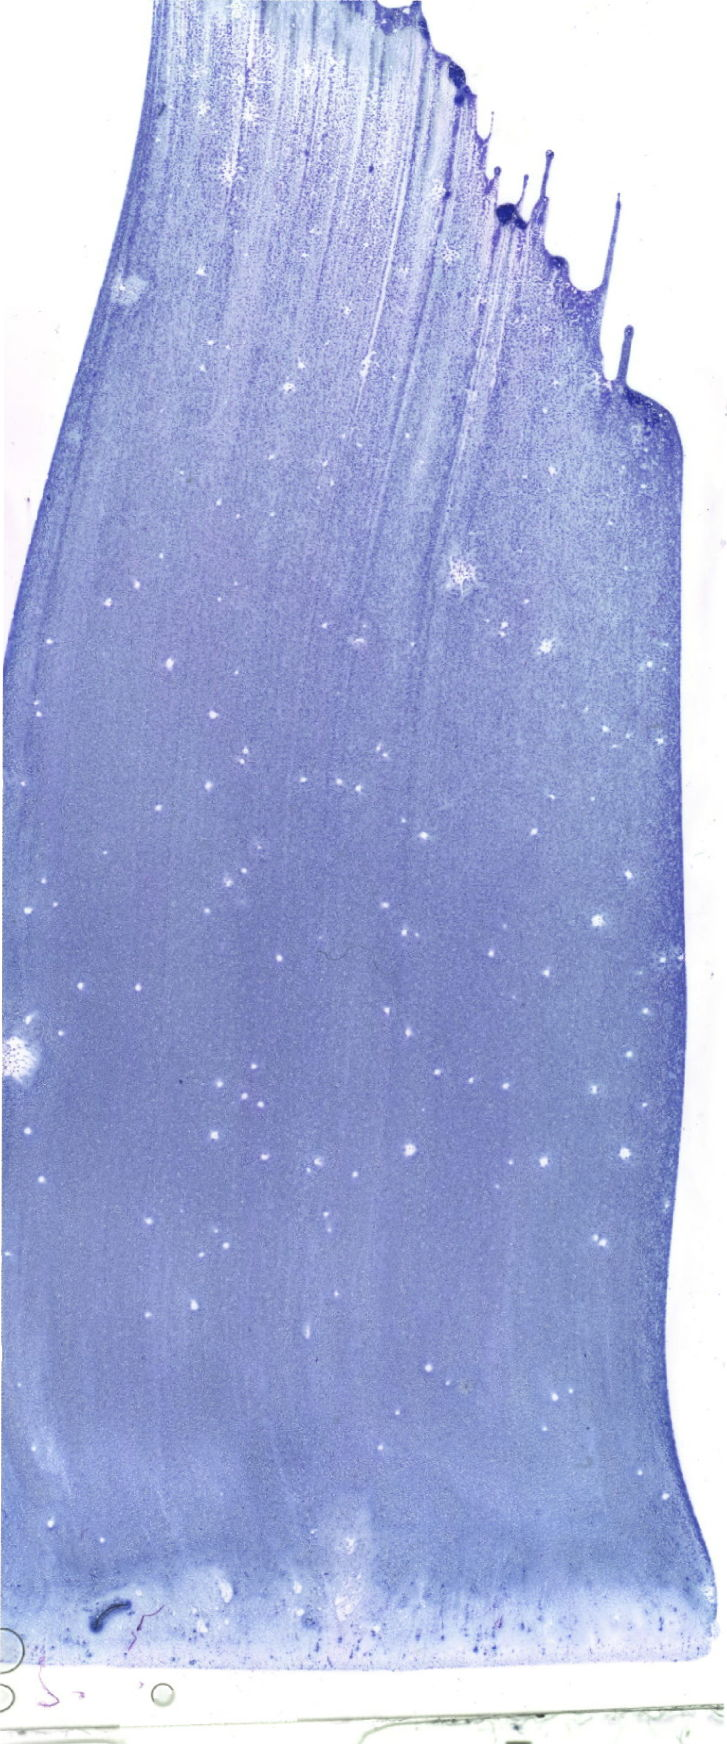
Bone marrow aspirate smear, May-Grünwald–Giemsa stain, whole-slide image, whole scanned area (about 20.6 x 49.4 mm) shown as a low-resolution overview. Patient sex: female.
Diagnosis: Acute Monocytic Leukemia.